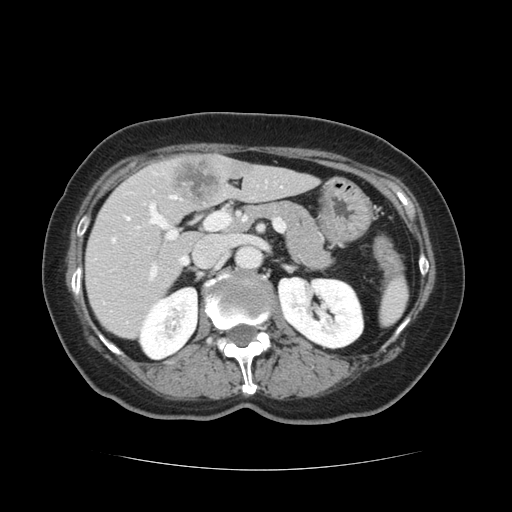
Contrast-enhanced abdominal CT, one axial slice; slice 63 of 128 in the series (ordered by position); 120 kVp; intravenous contrast given; soft-tissue window (W 400 / L 40 HU); 2.5 mm slice thickness; 512 × 512 image matrix, field of view 366 × 366 mm. Female patient, age 67 years. From the clinical record (not read from this slice): diagnosis: colorectal cancer liver metastases, imaged before liver resection; multiple liver metastases: yes; largest metastasis: 3 cm; chemotherapy before resection: no.
Annotated regions visible in this slice (expert manual segmentation):
- hepatic veins: box from (x=114, y=196) to (x=187, y=264) px
- liver: (x=86, y=155)–(x=316, y=339)
- planned liver remnant (the part of the liver to remain after resection): (x=86, y=164)–(x=315, y=339)
- portal vein (with intrahepatic branches): (x=112, y=181)–(x=268, y=281)
- liver metastasis: (x=172, y=159)–(x=220, y=204)